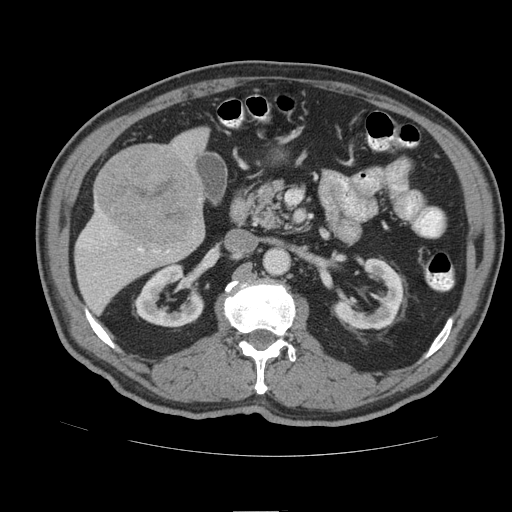
Contrast-enhanced abdominal CT (liver protocol), one axial slice; position 38 of 105 along the scan axis; reconstruction kernel STANDARD; soft-tissue window (W 400 / L 40 HU); 2.5 mm slice thickness; 512 × 512 image matrix, field of view 380 × 380 mm. From the clinical record (not read from this slice): diagnosis: hepatocellular carcinoma (patient treated with transarterial chemoembolisation; whether this scan precedes or follows treatment is not stated here); TNM stage (as recorded): Stage-IIIB; Child-Pugh class: A; tumour nodularity: multinodular.
Outlined on this slice (semi-automatically segmented with operator editing):
- liver parenchyma outside the tumour (the mass and vessels are separate outlines, so this box may not span the whole liver): bounding box <74,126,208,313> (left, top, right, bottom; pixels)
- mass: <96,147,201,248>
- liver vessels: <84,239,169,253>